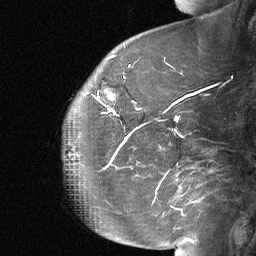
Breast MRI (dynamic contrast-enhanced), one sagittal slice; slice 20 of 64 in the series (ordered by position); dynamic contrast-enhanced study with each time point stored as its own series, time point 2 of 3 at this slice position (early post-contrast, ordered by acquisition time); 1.5 T; TE 4.8 ms, TR 27 ms; 2 mm slice thickness; 256 × 256 image matrix, field of view 200 × 200 mm. Female patient, age 60 years. Case-level facts recorded for this patient, not image findings: setting: breast cancer imaged before/during neoadjuvant chemotherapy; receptor status: HR-positive, HER2-negative.
Outlined on this slice (semi-automatically segmented with operator editing):
- analysis volume of interest (the breast-tissue region the enhancement analysis was run in; not a lesion): bounding box (x1, y1, x2, y2) in pixels: (92, 70, 134, 112)
- tumour enhancement mask (voxels above the 90 % enhancement threshold inside the analysis volume of interest): (94, 89, 114, 111)